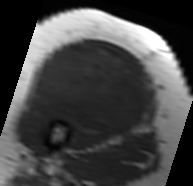
MRI of an extremity soft-tissue mass, one axial slice; position 39 of 91 along the scan axis; MR volume resampled by the dataset authors to the PET/CT grid (not the native acquisition matrix); 193 × 186 image matrix, field of view 188 × 182 mm. Female patient. Case-level facts recorded for this patient, not image findings: histological type: malignant solitary fibrous tumor; grade: intermediate; site of the primary tumour: right thigh.
Annotated regions visible in this slice (expert contour drawn on MRI and transferred to this co-registered scan by the dataset authors):
- gross tumour volume including surrounding oedema: bounding box [x1, y1, x2, y2] px = [26, 42, 153, 139]
- gross tumour volume (mass): [31, 42, 148, 136]